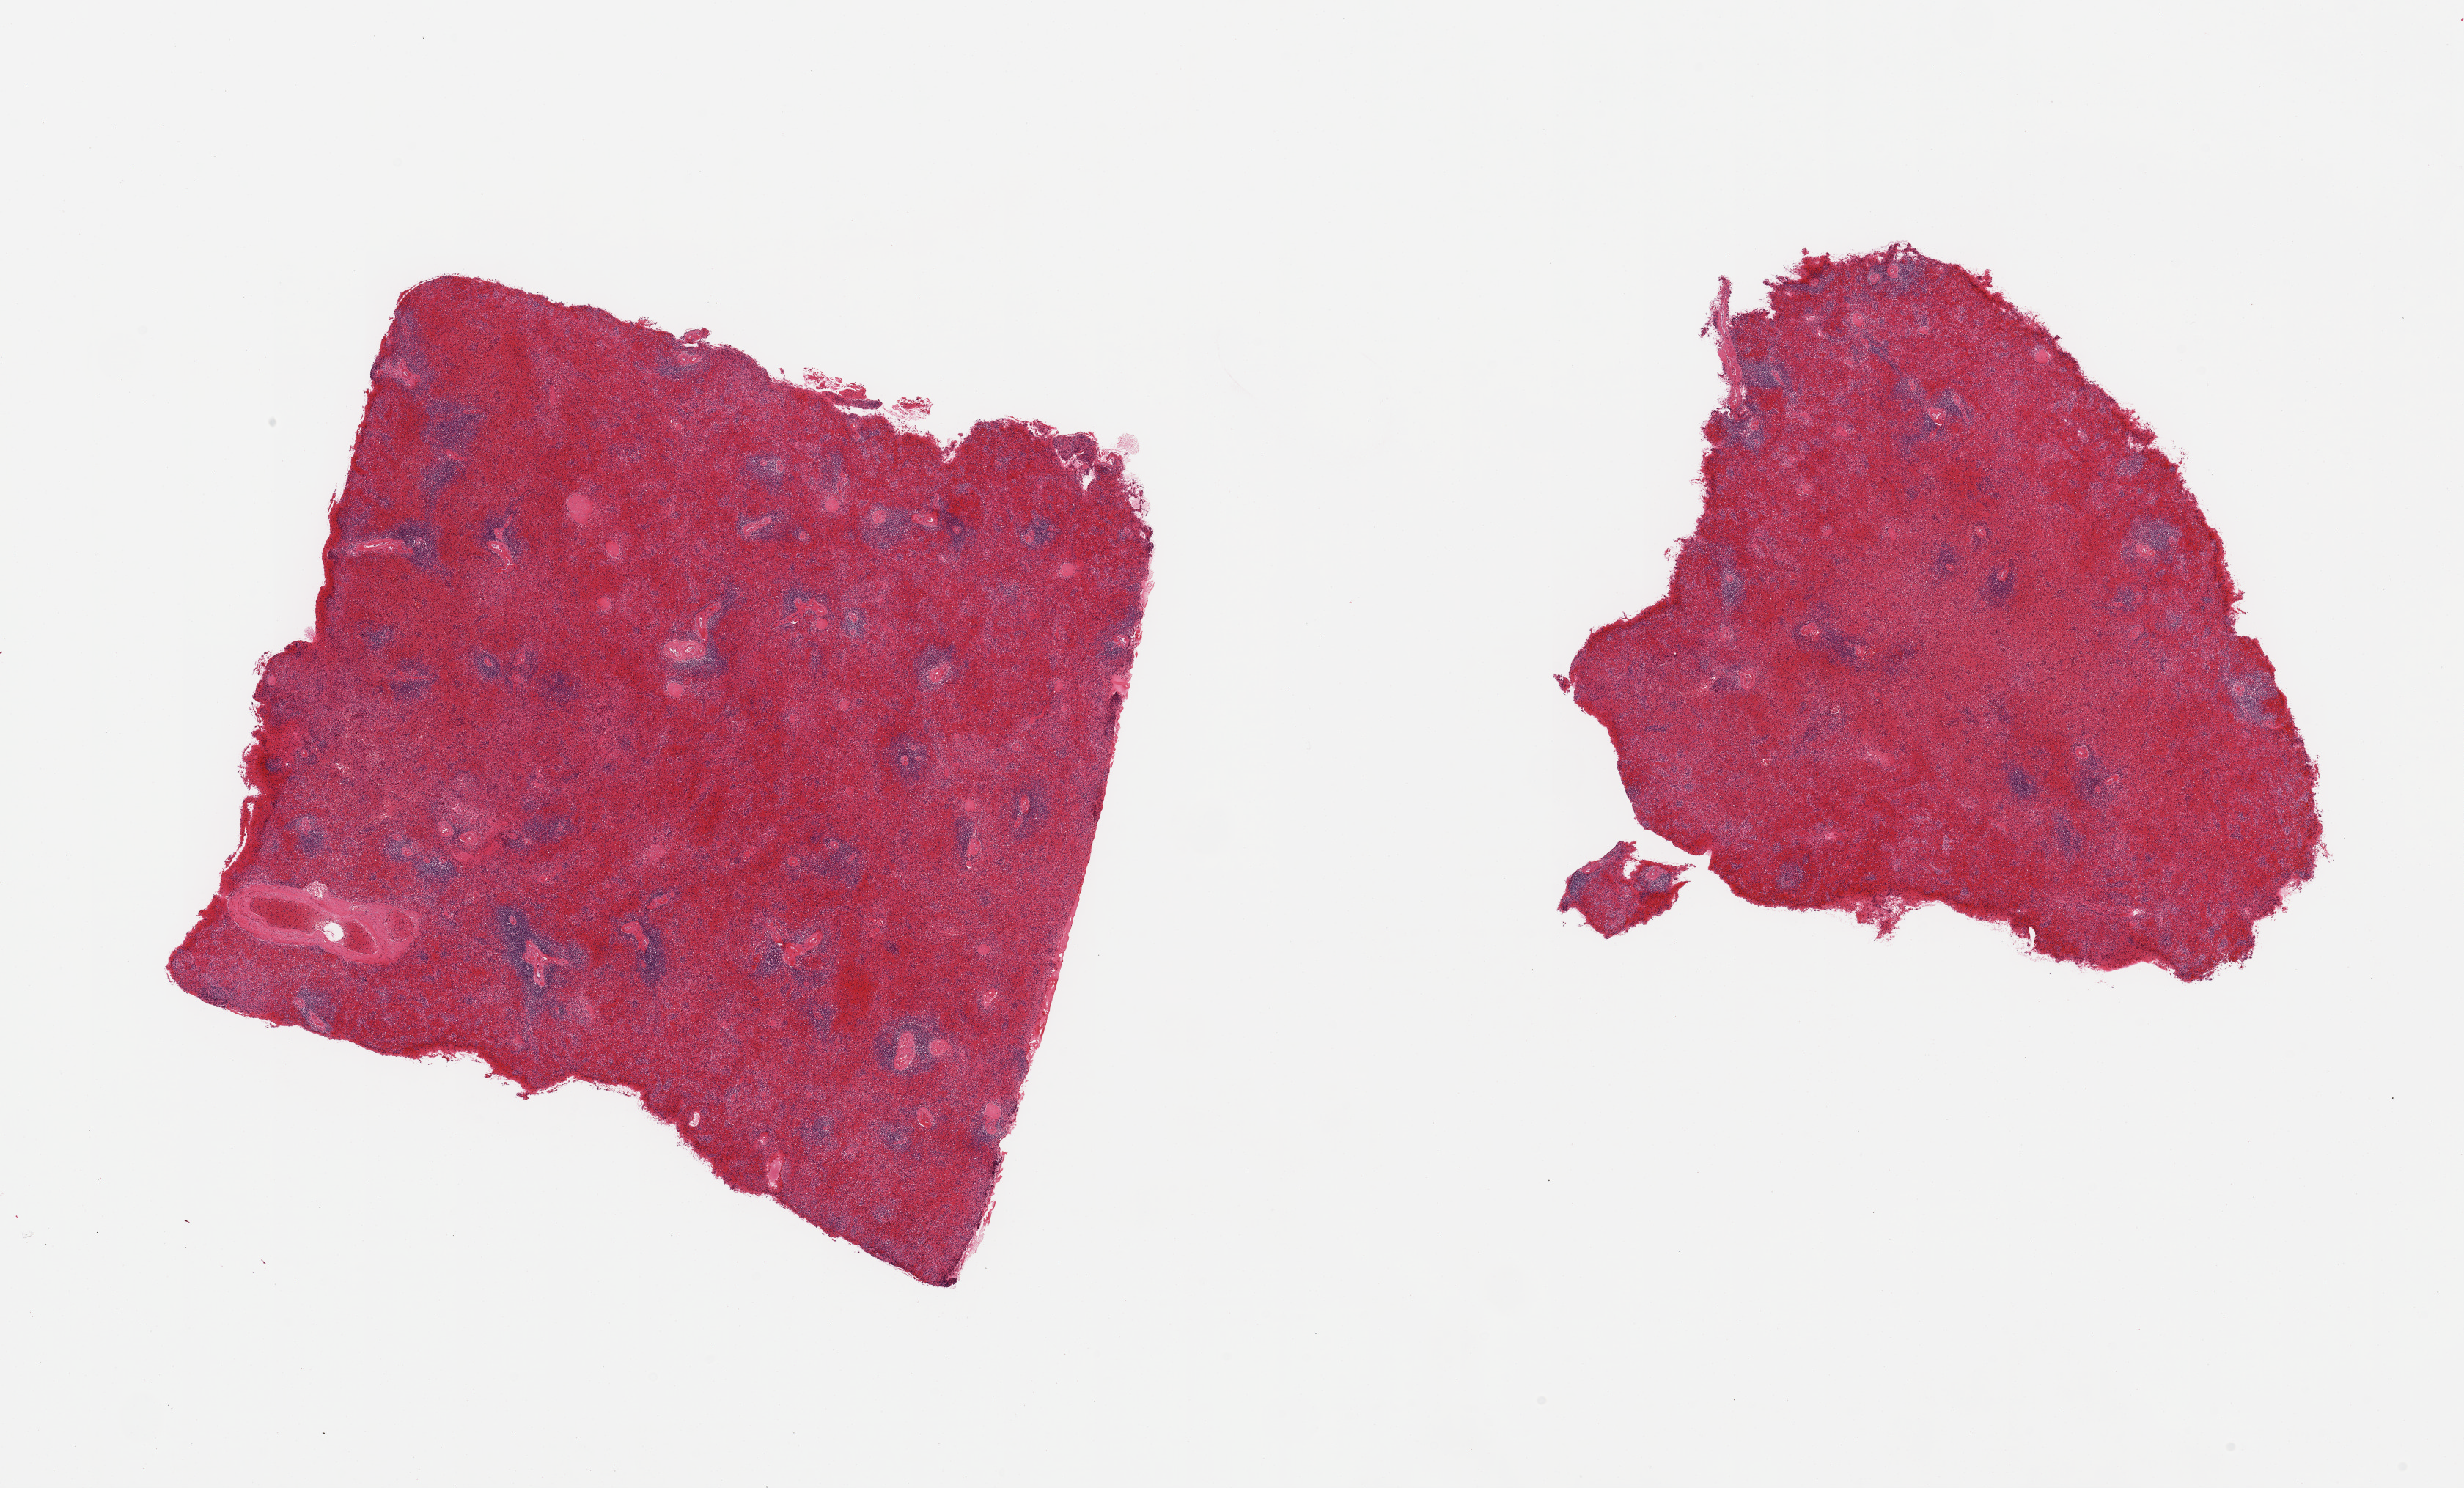
Digitized haematoxylin and eosin-stained section — low-resolution overview of the scanned area, about 26.6 x 16.1 mm (from a 20x scan); PAXgene-fixed, paraffin-embedded tissue; section of spleen (target tissue); donor tissue sample. Male donor.
Reviewer comment on this tissue sample: 2 pieces; congested.